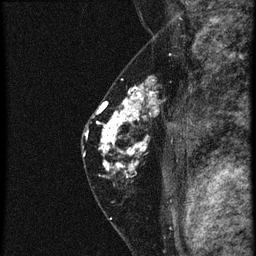
Breast MRI (dynamic contrast-enhanced), one sagittal slice. Position 39 of 60 along the scan axis. 4 images stored at this slice position (order not interpretable as contrast timing). 1.5 T. TE 4.2 ms, TR 20.4 ms. 1.5 mm slice thickness. 256 × 256 image matrix, field of view 180 × 180 mm. Female patient, age 46 years. From the clinical record (not read from this slice): setting: breast cancer imaged before/during neoadjuvant chemotherapy; receptor status: triple-negative.
Structures marked on this image (semi-automatically segmented with operator editing):
- analysis volume of interest (the breast-tissue region the enhancement analysis was run in; not a lesion): bounding box <88,82,181,185> (left, top, right, bottom; pixels)
- tumour enhancement mask (voxels above the 90 % enhancement threshold inside the analysis volume of interest): <100,82,157,175>